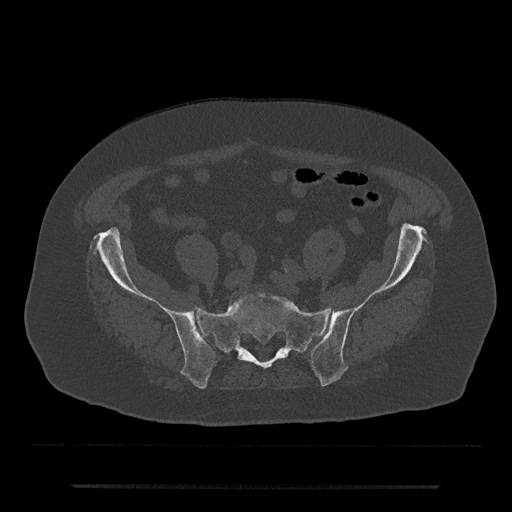
CT including the spine, one axial slice. Slice 232 of 797 in the series (ordered by position). Reconstruction kernel Br40s/3. 120 kVp. Bone window (W 1800 / L 400 HU). 512 × 512 image matrix, field of view 434 × 434 mm. Patient: male, 80 years. Case-level facts recorded for this patient, not image findings: primary cancer: prostate.
Annotated regions visible in this slice (semi-automatic segmentation, software-assisted and operator-edited):
- L5 vertebra: box from (x=236, y=293) to (x=287, y=303) px